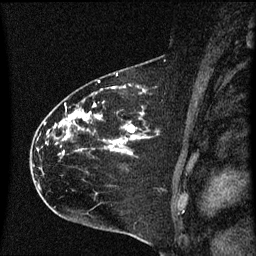
Breast MRI (dynamic contrast-enhanced), one sagittal slice; slice 41 of 60 in the series (ordered by position); dynamic contrast-enhanced series, image 2 of 3 at this slice position (ordered by acquisition); 1.5 T; TE 4.2 ms, TR 8.4 ms; 2 mm slice thickness; 256 × 256 image matrix, field of view 200 × 200 mm. Patient: female, 35 years. Case-level facts recorded for this patient, not image findings: setting: breast cancer imaged before/during neoadjuvant chemotherapy; receptor status: HER2-positive.
Annotated regions visible in this slice (semi-automatic segmentation, software-assisted and operator-edited):
- analysis volume of interest (the breast-tissue region the enhancement analysis was run in; not a lesion): bounding box (x1, y1, x2, y2) in pixels: (32, 68, 174, 173)
- tumour enhancement mask (voxels above the 70 % enhancement threshold inside the analysis volume of interest): (54, 74, 142, 155)